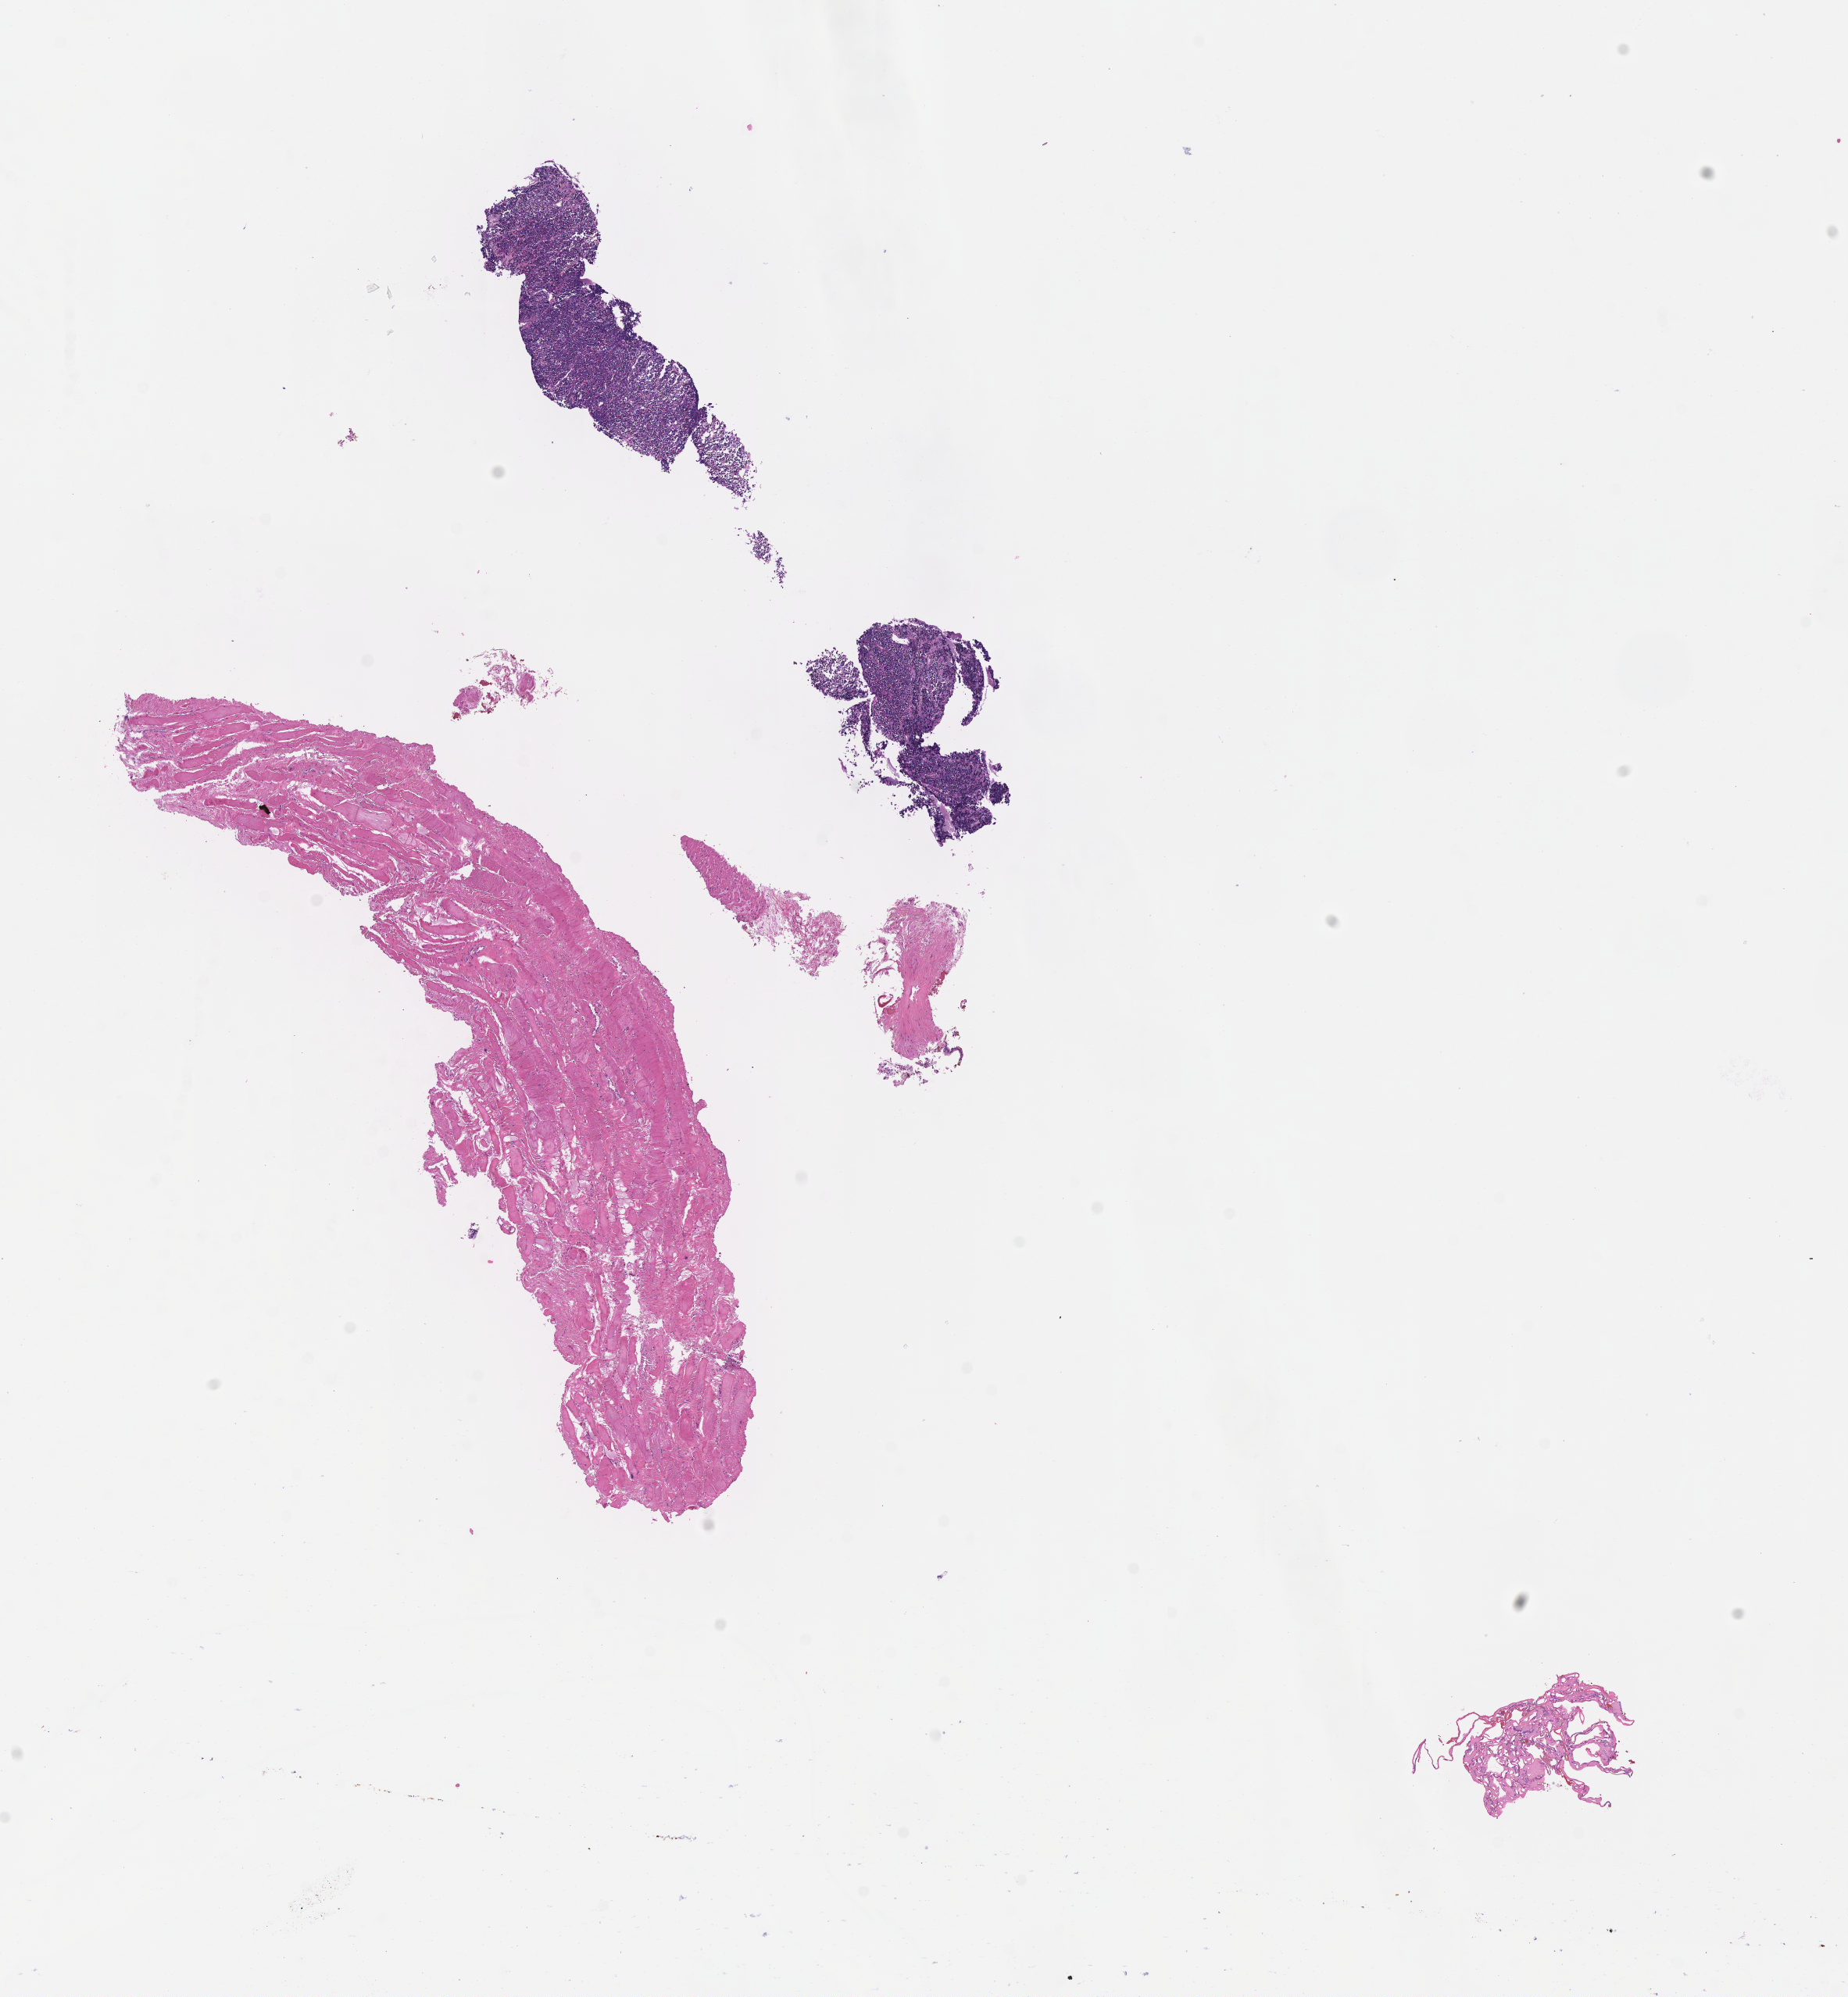
Whole-slide image, haematoxylin and eosin stain, a low-resolution overview of the entire scanned area, about 9.6 x 10.3 mm; formalin-fixed, paraffin-embedded (FFPE) tissue; primary tumor; anatomic site: liver. Patient sex: male. Pathologist review of this section (percent, as recorded): tumor cells 35%, tumor nuclei 80%, stromal cells 65%, necrosis 0%, normal cells 0%. Inflammatory infiltration, as recorded: lymphocyte infiltration 25%, monocyte infiltration 20%, neutrophil infiltration 5%.
Section: top of the tissue portion. Histologic diagnosis: Burkitt lymphoma, NOS.